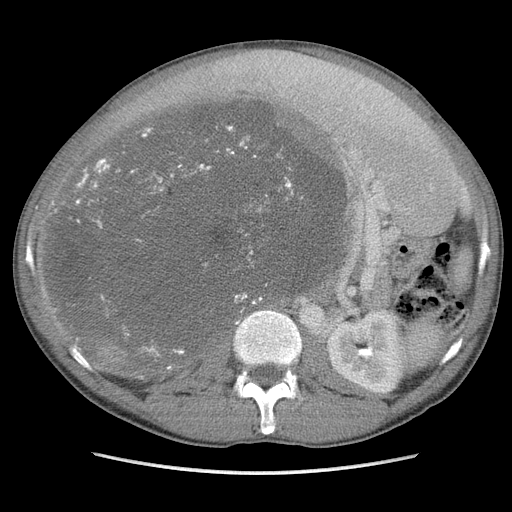
Contrast-enhanced abdominal CT, one axial slice. Slice 60 of 115 in the series (ordered by position). Soft-tissue window (W 400 / L 40 HU). 5 mm slice thickness. 512 × 512 image matrix, field of view 360 × 360 mm. Male patient. From the clinical record (not read from this slice): diagnosis: adrenocortical carcinoma; tumour side: right adrenal; Ki-67 index: 13 %; stage (as recorded): 3.
Annotated regions visible in this slice (semi-automatic segmentation, software-assisted and operator-edited):
- mass: bounding box <50,97,340,371> (left, top, right, bottom; pixels)